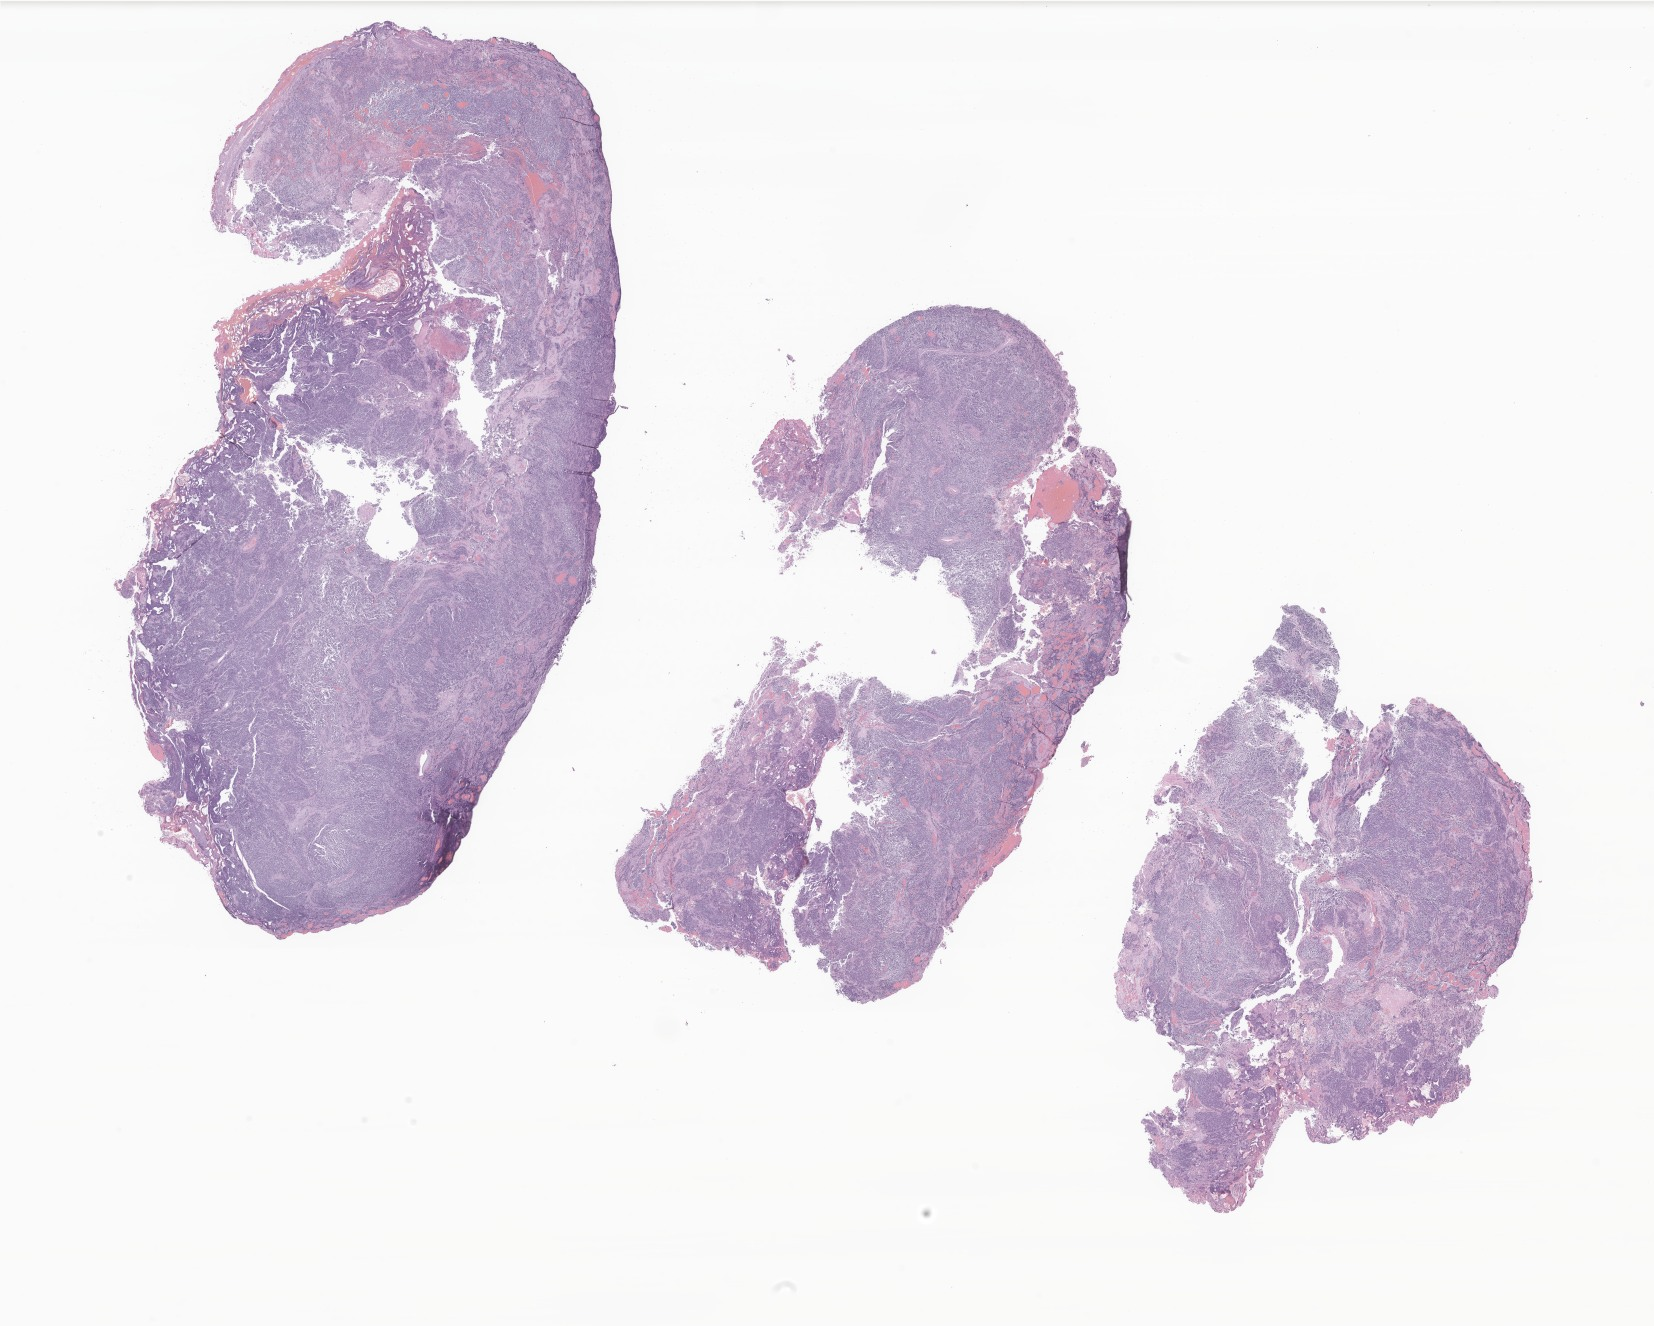
Hematoxylin and eosin (H&E) whole-slide image of tumor tissue from the brain — whole scanned area (about 27.9 x 22.4 mm) shown as a low-resolution overview; formalin-fixed paraffin-embedded section. Patient male; age 33 months (2 years 9 months).
Recorded diagnosis: Medulloblastoma, NOS.